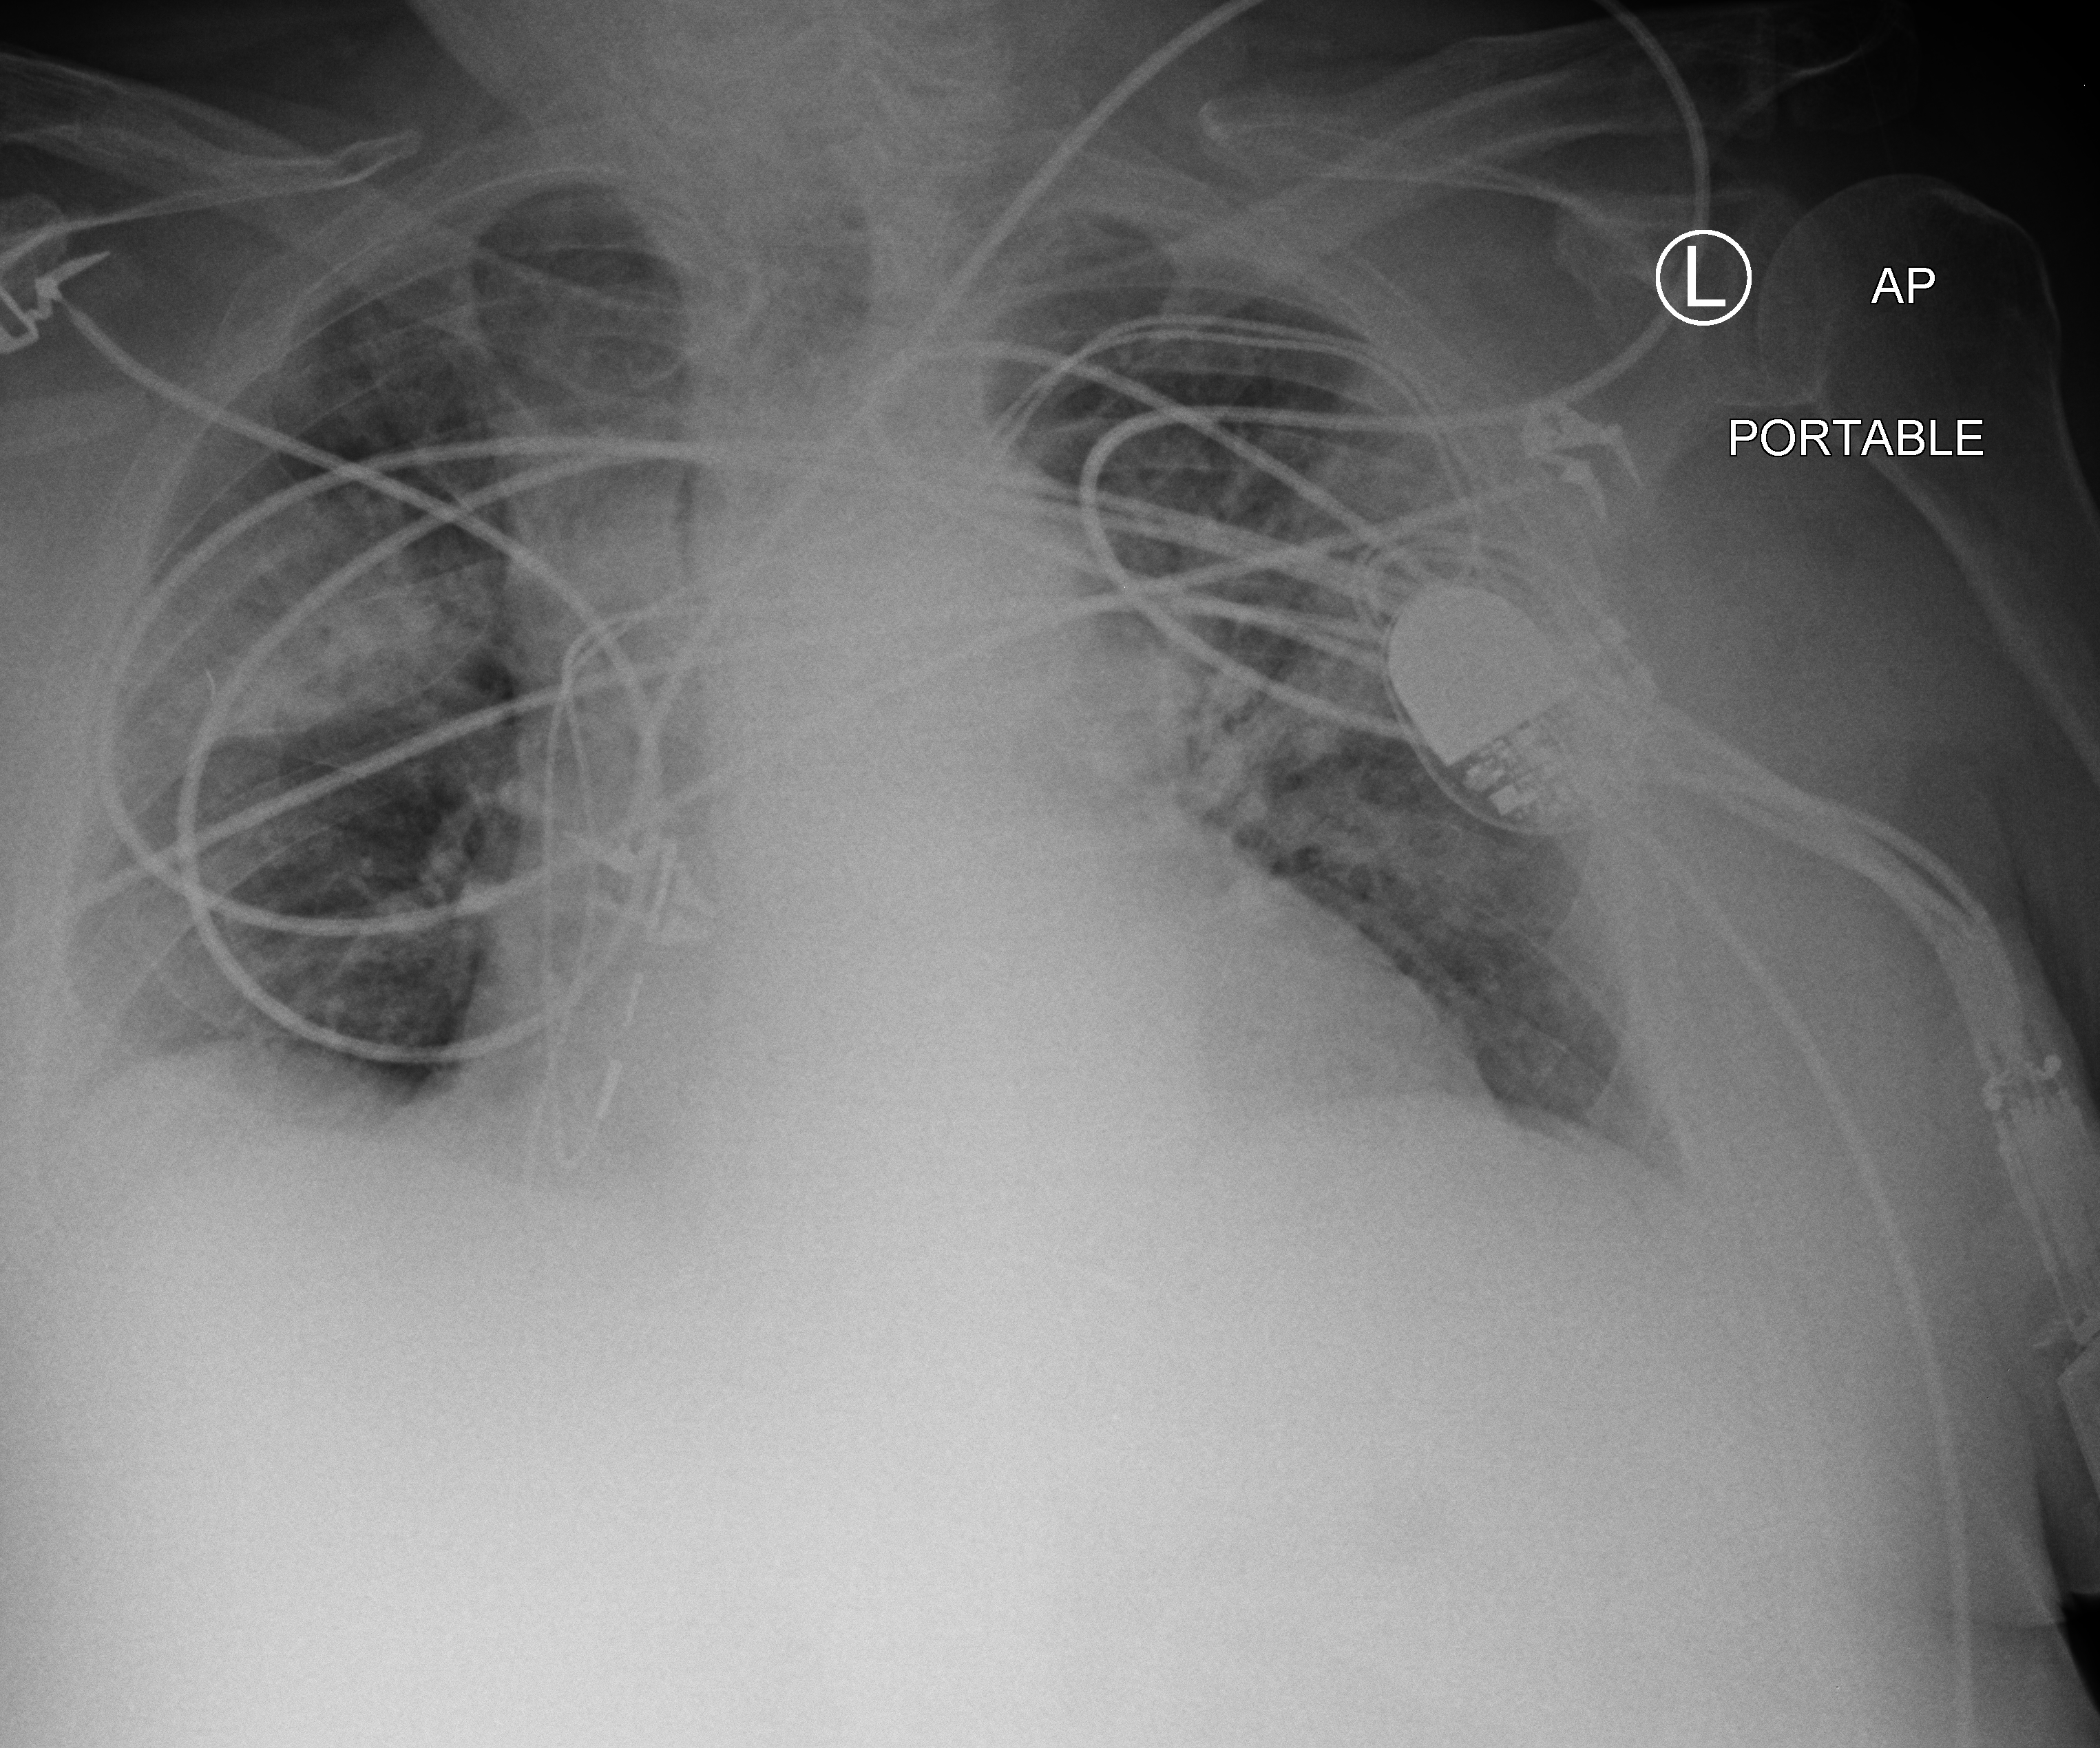
Portable chest radiograph. Patient hospitalised with COVID-19; male, aged 75–90 years.
Admission-level facts for this patient (not findings on this image; timing relative to this image not recorded): mechanically ventilated during this hospital stay: no; admitted to intensive care during this hospital stay: no; COPD (admission record): yes.